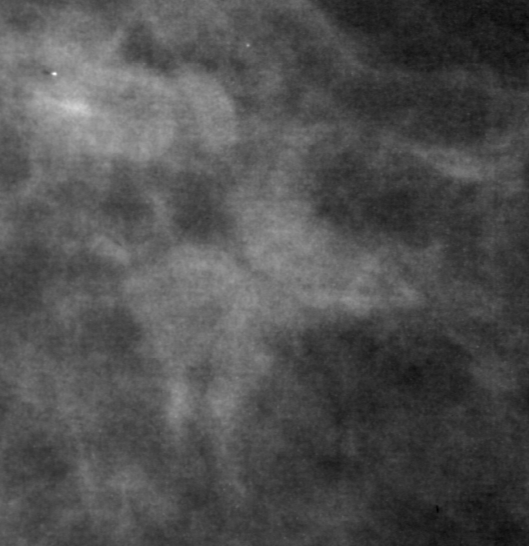
Region of interest cut from a scanned film mammogram (one marked finding), right breast, MLO view.
Mass, shape irregular, margins ill defined; BI-RADS assessment category 4; pathology result (as recorded, not read from the image): malignant.